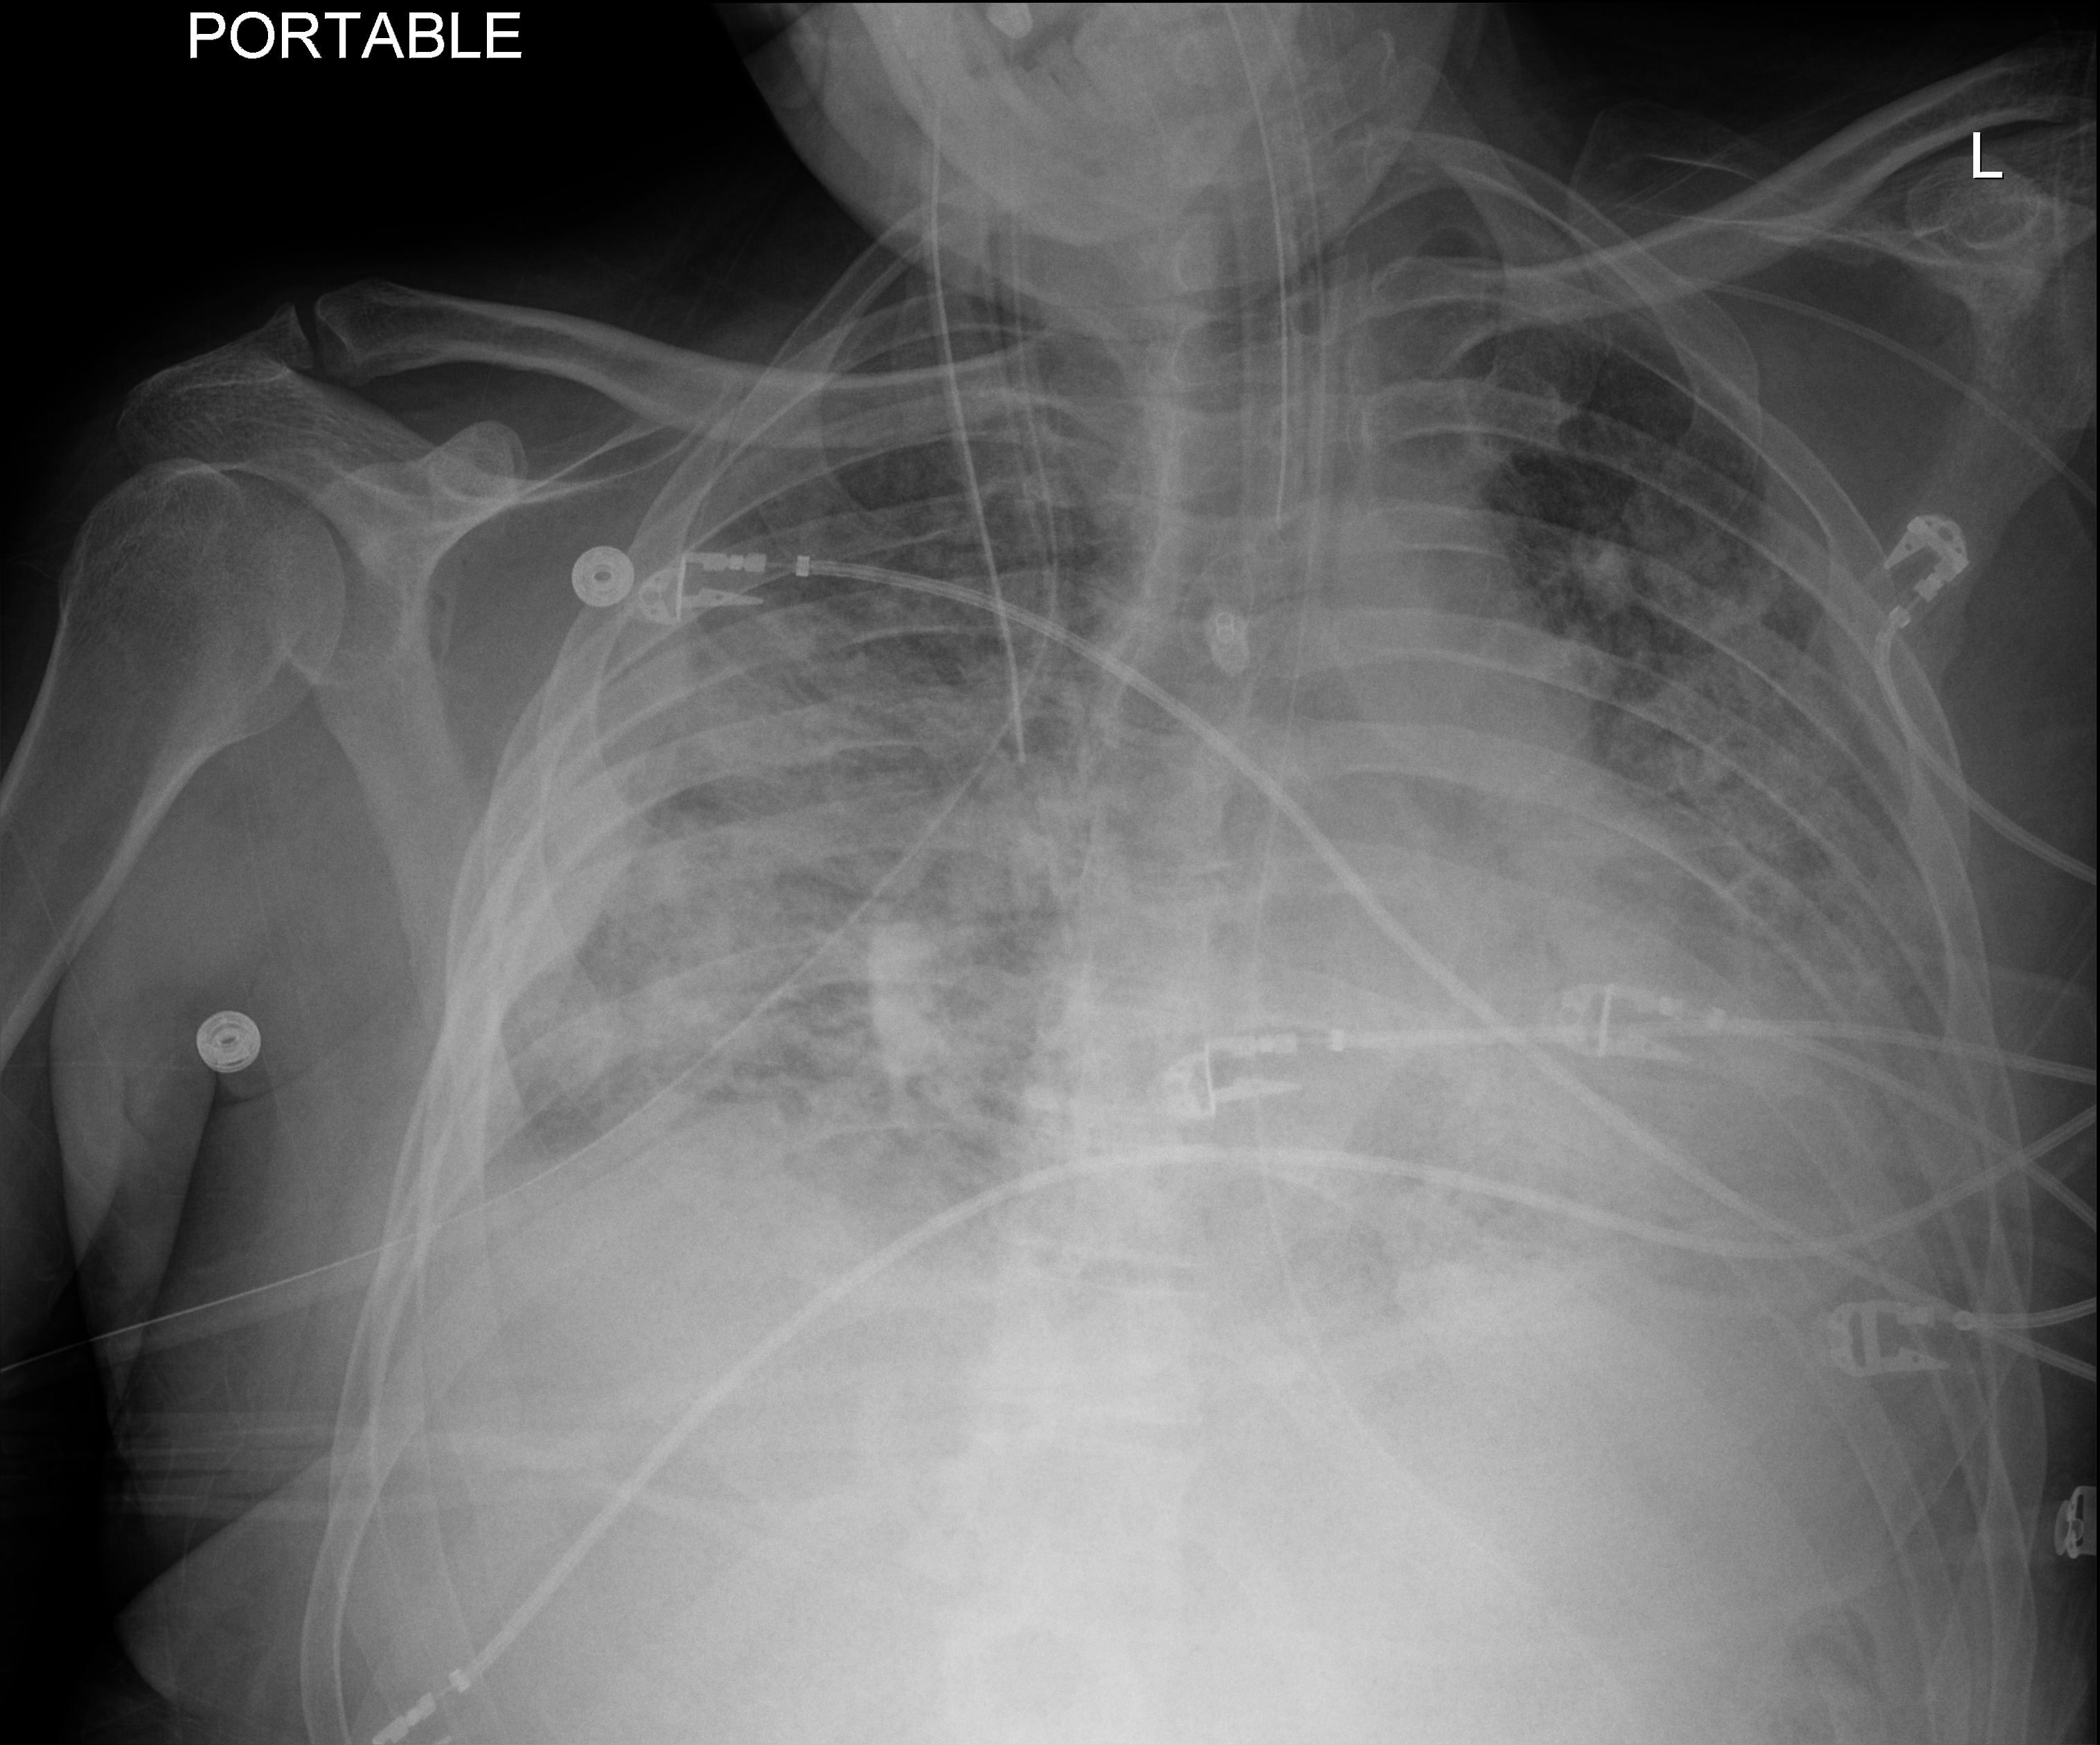
Chest X-ray (portable); anteroposterior (AP) projection. Male patient hospitalised with COVID-19, age 18–59 years.
Hospital-stay facts (about this admission, not read from this image; timing relative to this image not recorded): admitted to intensive care during this hospital stay: yes.